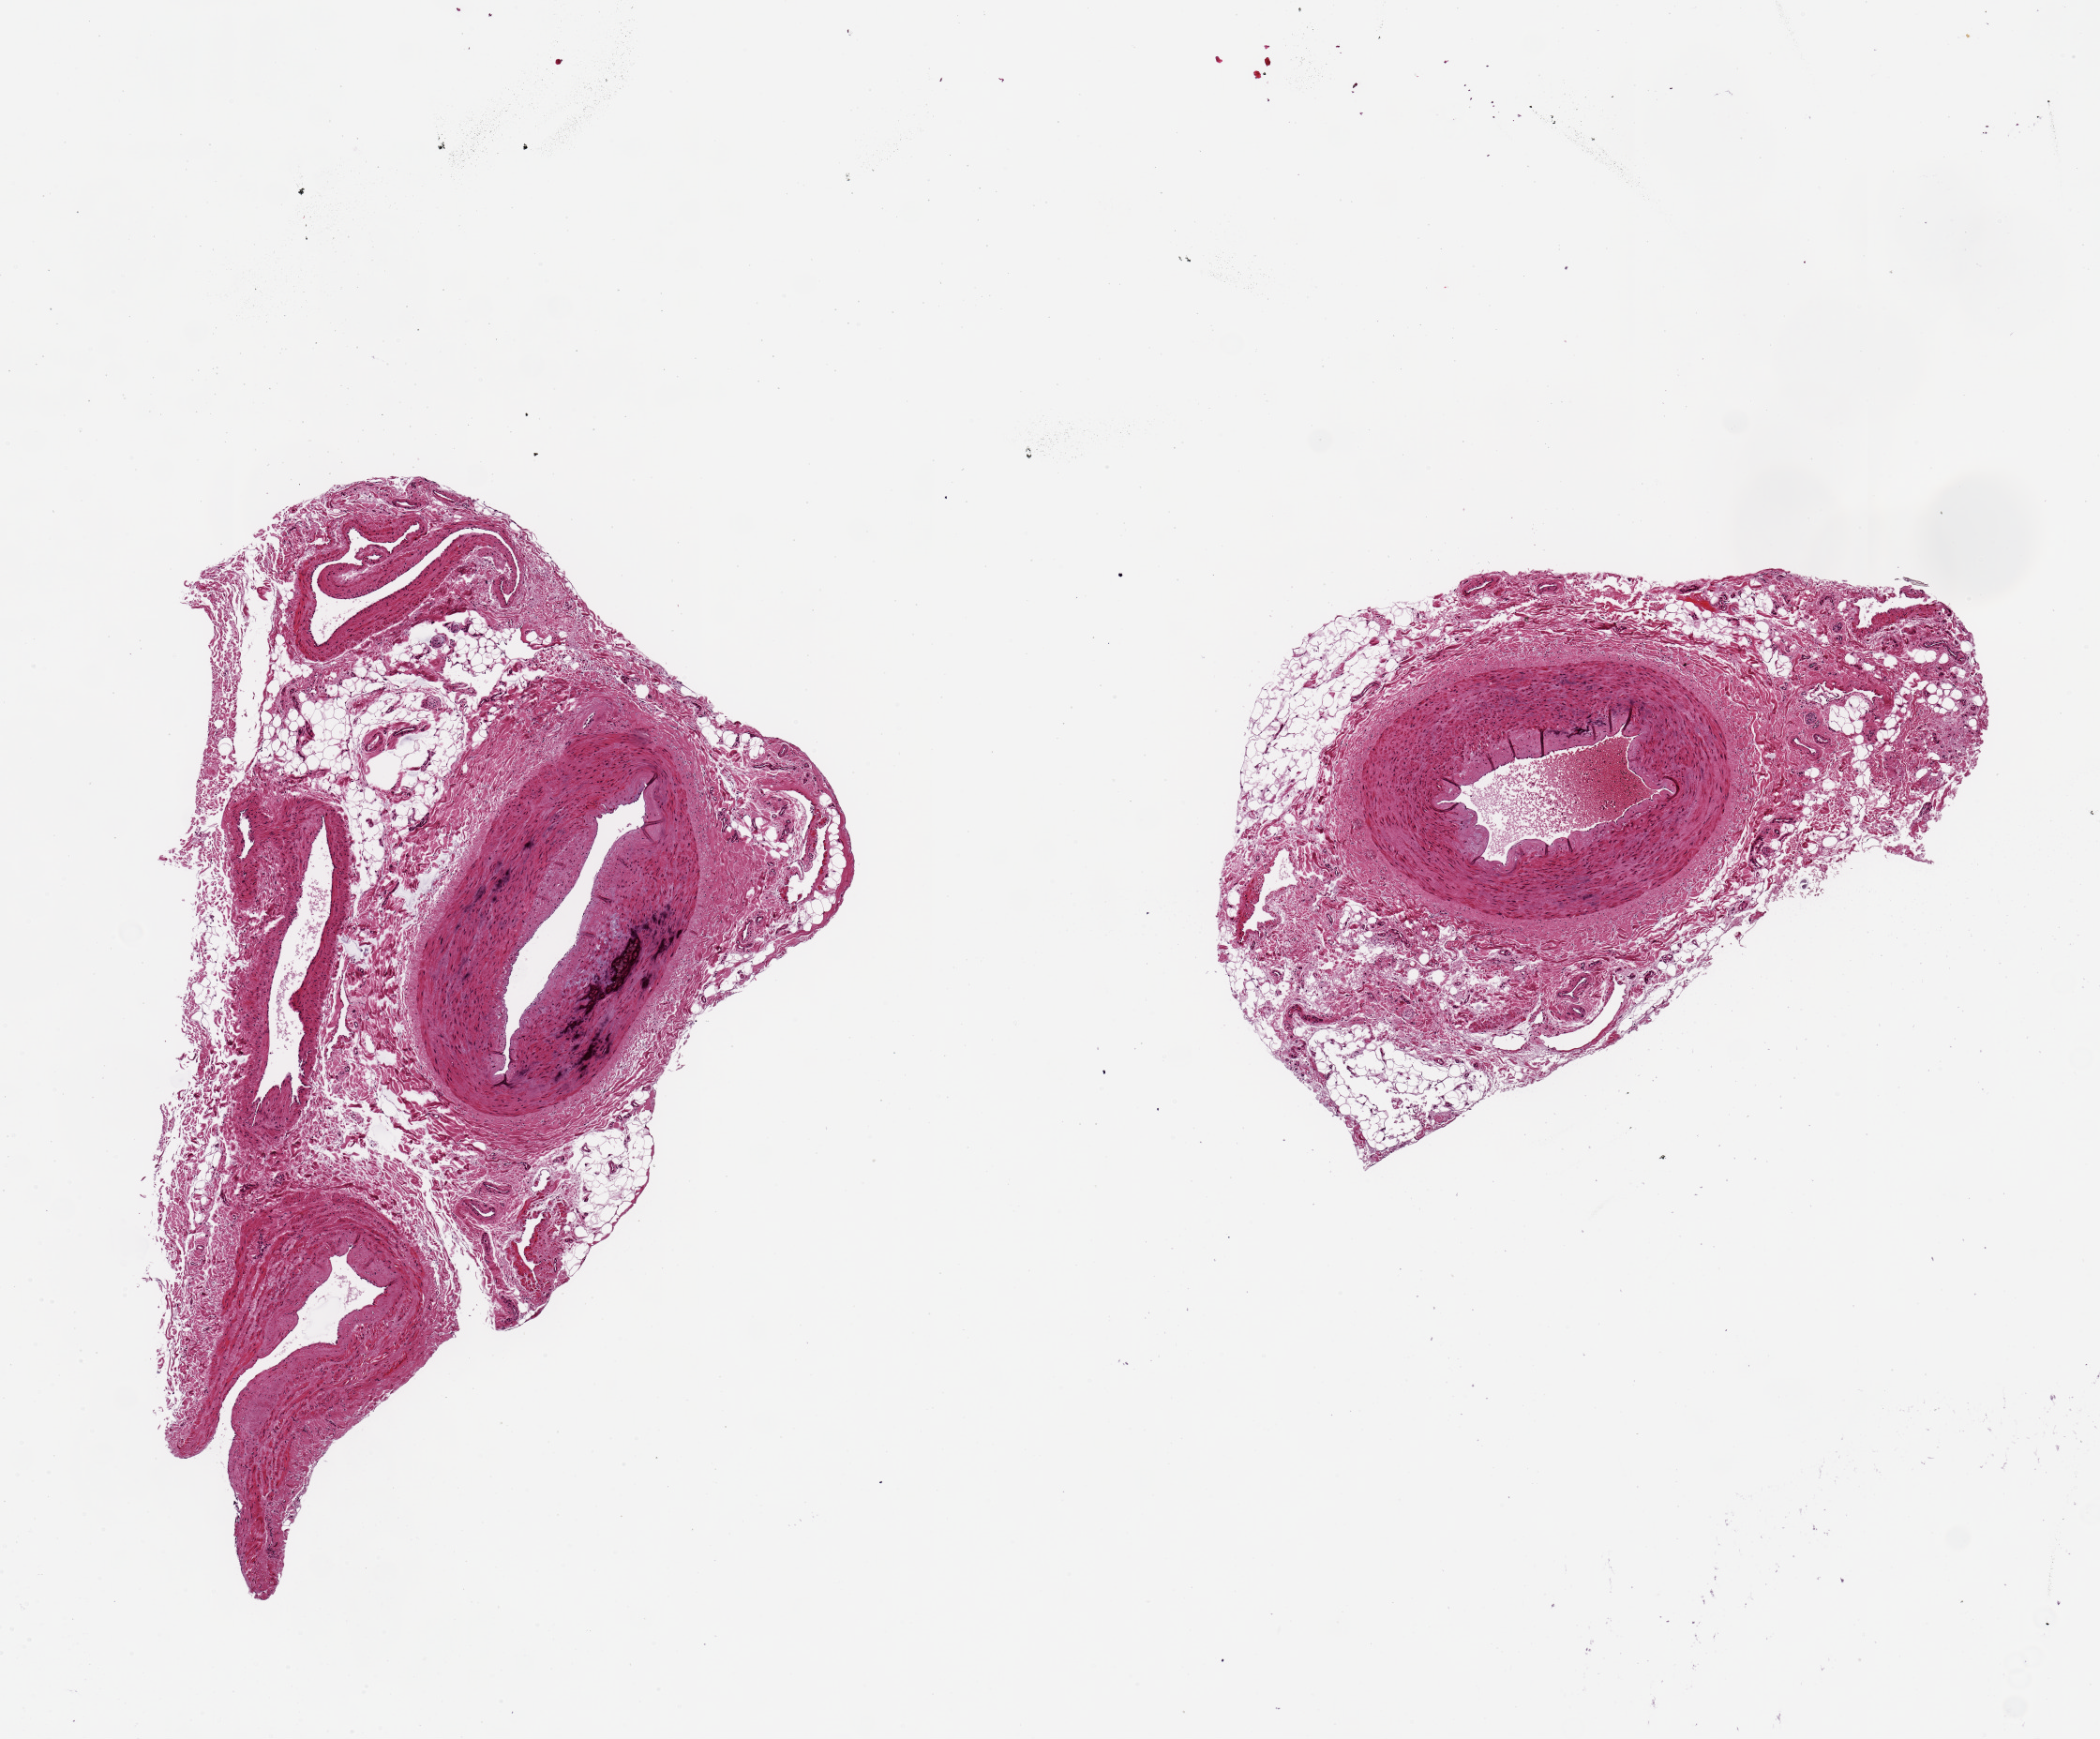
Hematoxylin and eosin (H&E) whole-slide image, brightfield, shown as a low-resolution overview of the whole scanned area (about 8.9 x 7.3 mm, slide scanned at 20x), PAXgene-fixed, paraffin-embedded tissue, sampled site (target tissue): tibial artery, tissue donor sample.
• pathologist's review note for this sample: 2 ~2x1mm aliquots, substantial rims of fat/fibrous tissue around both (up to 1-2mm)